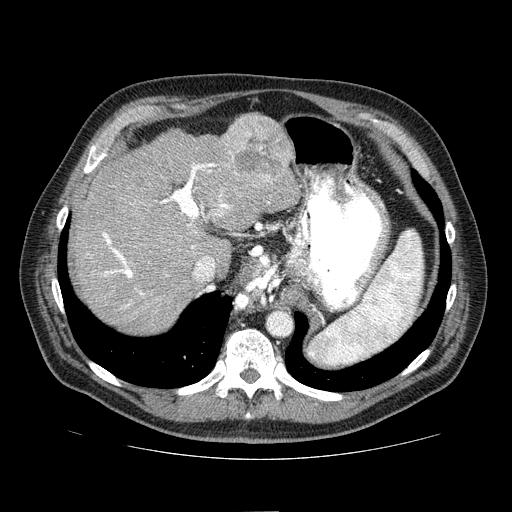
Contrast-enhanced abdominal CT (liver protocol), one axial slice; slice 55 of 81 in the series (ordered by position); one of 2 acquisitions stored at this slice position; soft-tissue window (W 400 / L 40 HU); 512 × 512 image matrix, field of view 400 × 400 mm. From the clinical record (not read from this slice): diagnosis: hepatocellular carcinoma (patient treated with transarterial chemoembolisation; whether this scan precedes or follows treatment is not stated here); TNM stage (as recorded): Stage-IIIA; Child-Pugh class: A; tumour size: 5.6 cm.
Annotated regions visible in this slice (semi-automatic segmentation, software-assisted and operator-edited):
- abdominal aorta: bounding box (x1, y1, x2, y2) in pixels: (269, 313, 292, 335)
- liver parenchyma outside the tumour (the mass and vessels are separate outlines, so this box may not span the whole liver): (70, 114, 300, 332)
- mass: (220, 115, 291, 187)
- liver vessels: (87, 163, 270, 308)